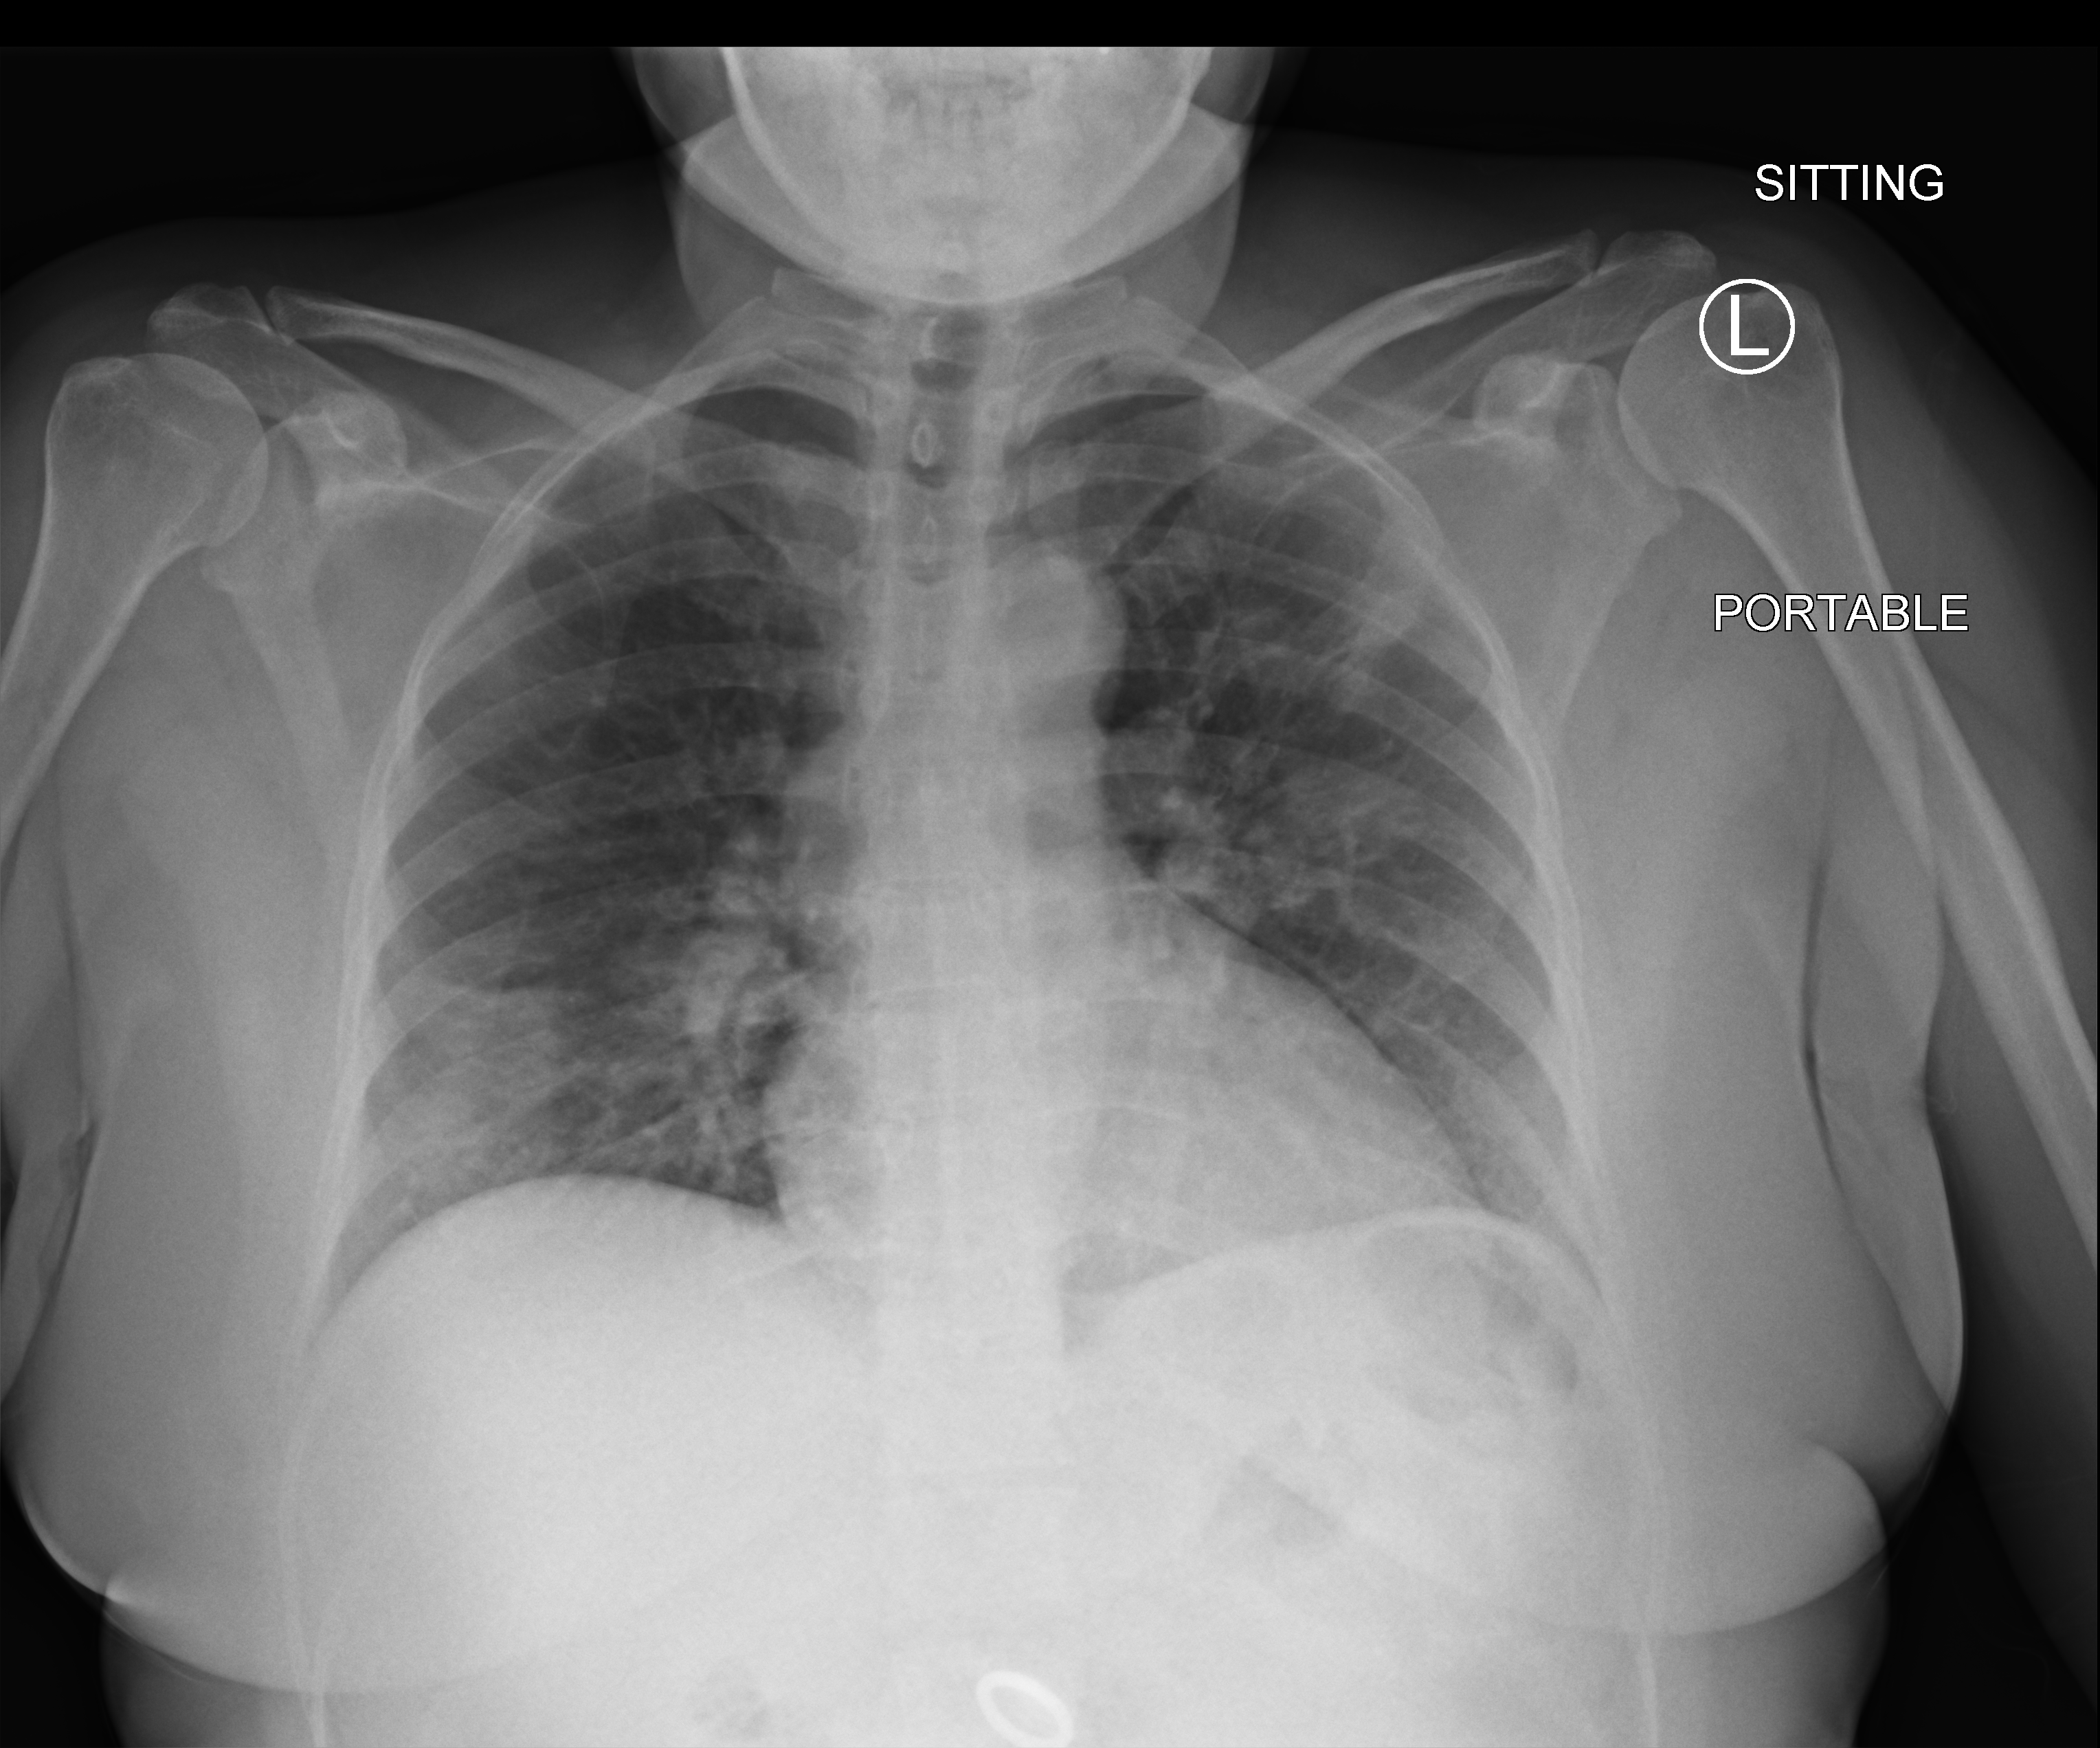
Bedside chest radiograph (computed radiography), anteroposterior (AP) projection. Female patient hospitalised with COVID-19, age 18–59 years.
From the hospital-stay record, not from the radiograph (when in the stay this image was taken is not recorded): length of hospital stay: 1 day; mechanically ventilated during this hospital stay: no; admitted to intensive care during this hospital stay: no.